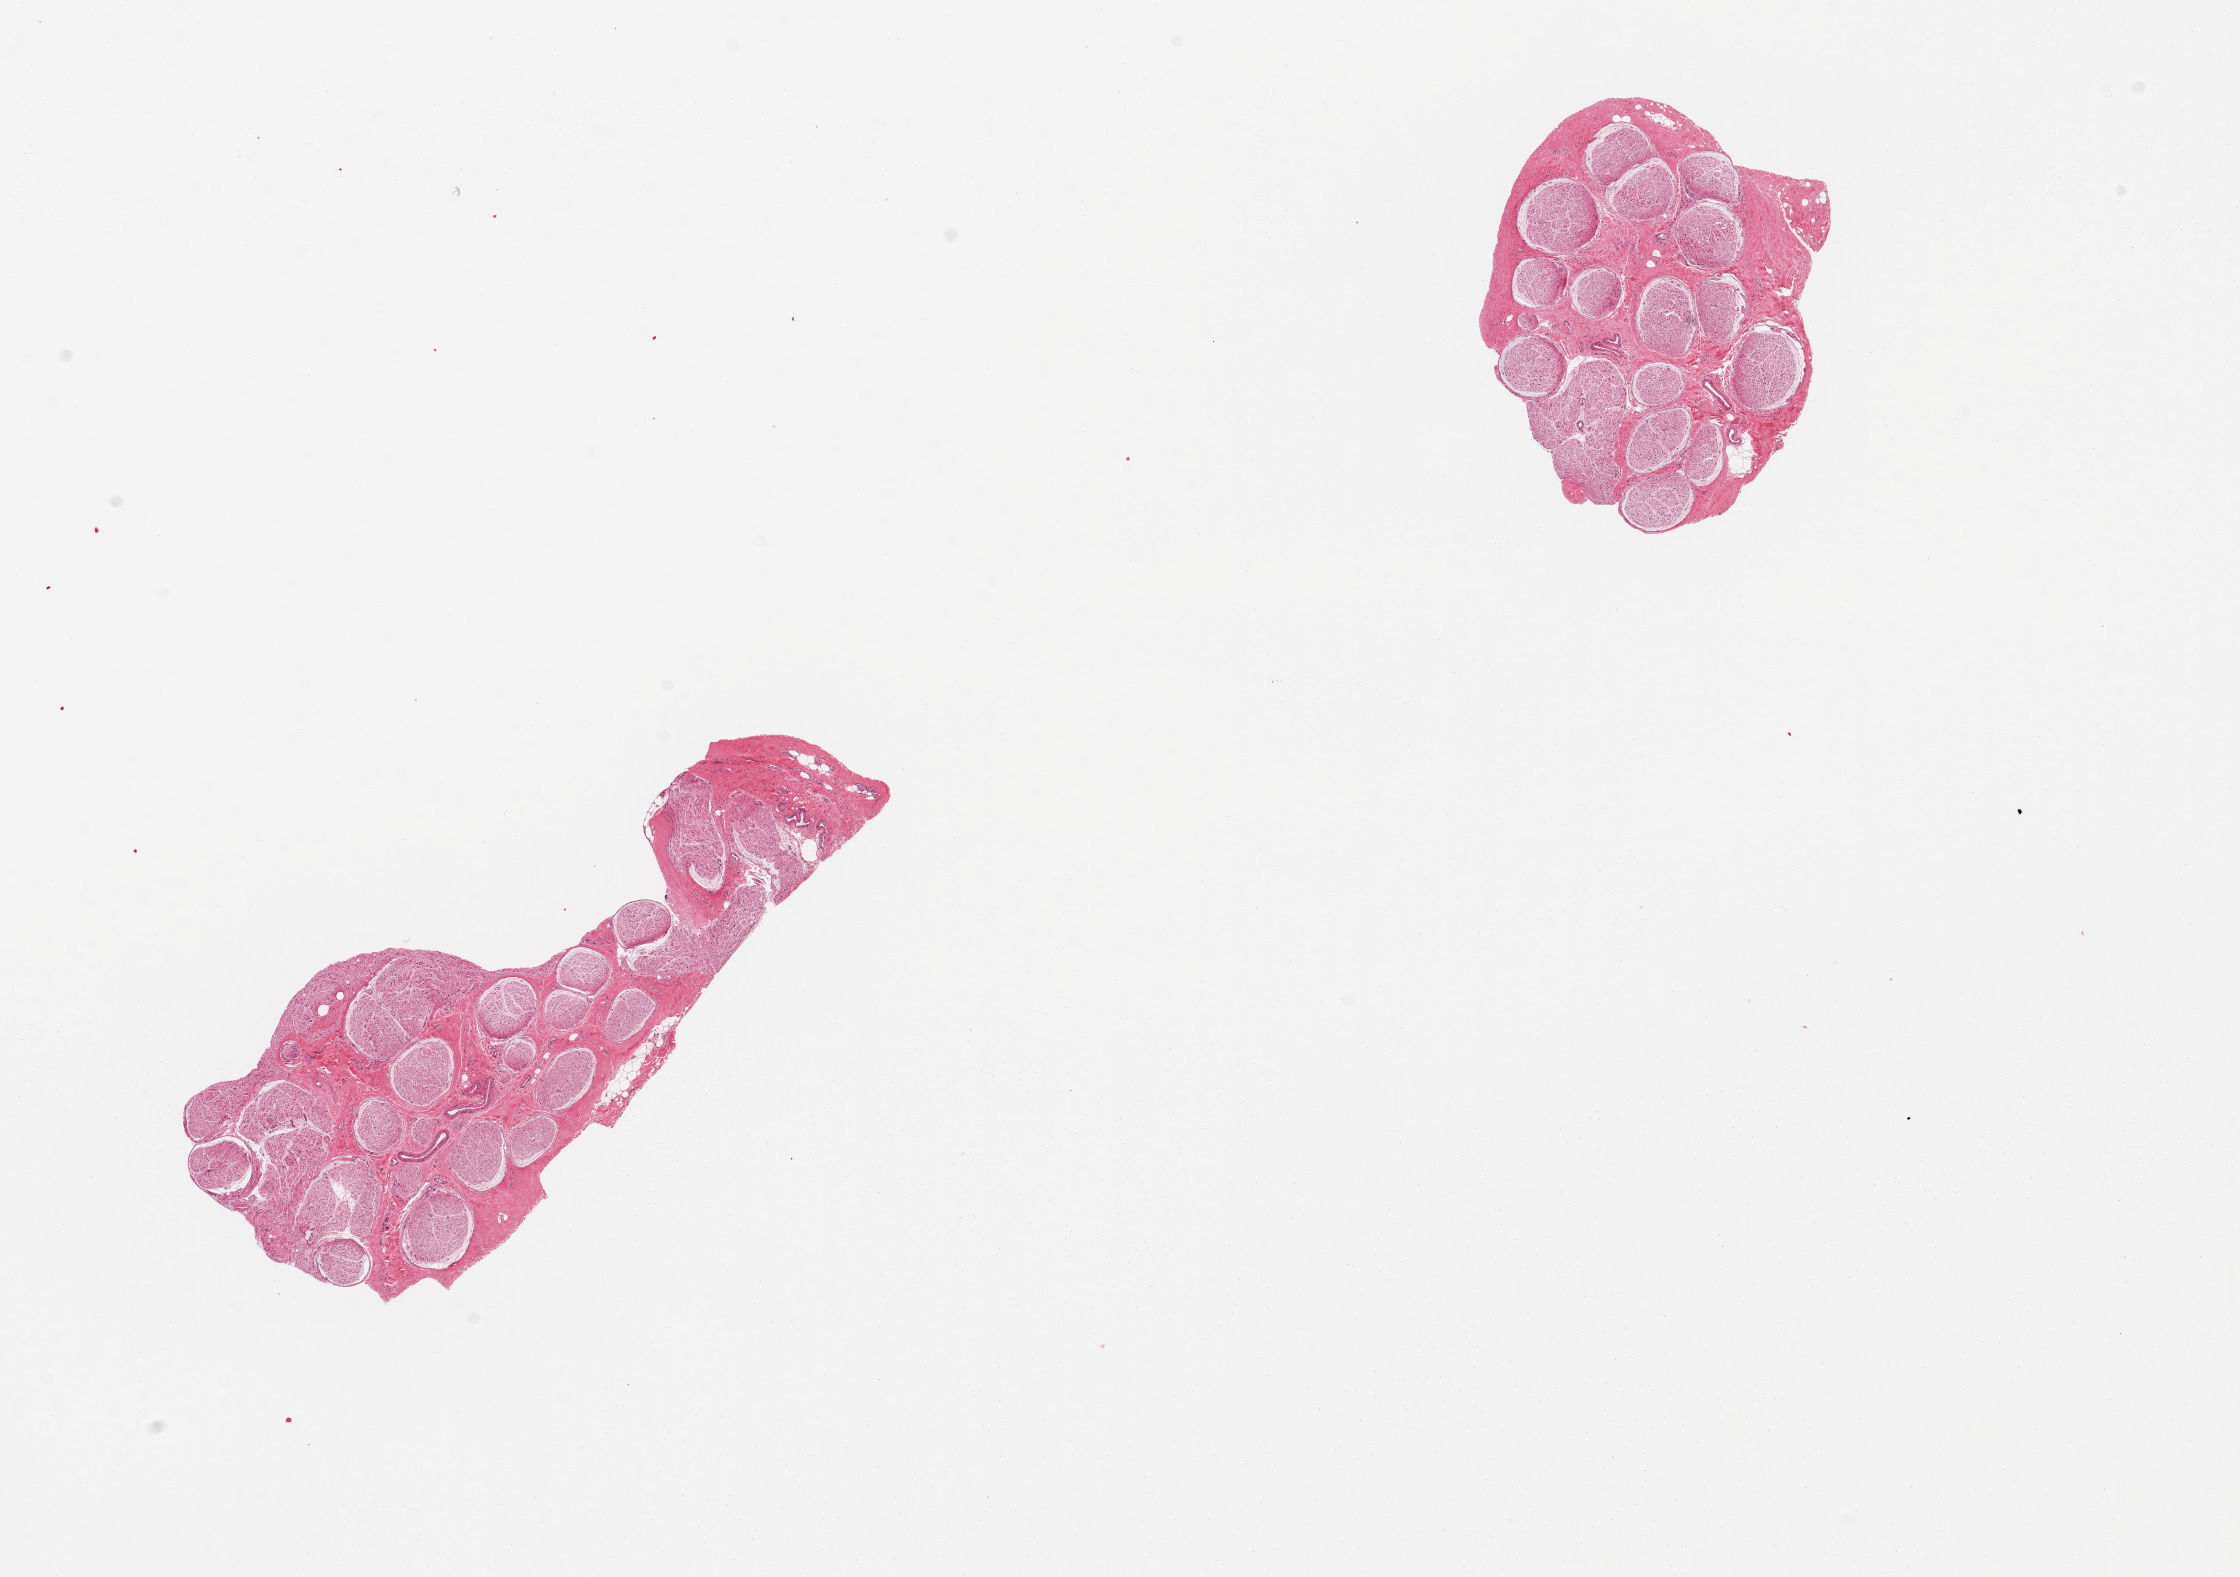
Whole-slide image, haematoxylin and eosin stain, shown as a low-resolution overview of the whole scanned area (about 17.7 x 12.5 mm, from a 20x scan). PAXgene-fixed paraffin-embedded (PFPE) section. Target tissue: tibial nerve. Tissue donor sample. Donor: female.
- review note (as recorded): 2 pieces, well trimmed